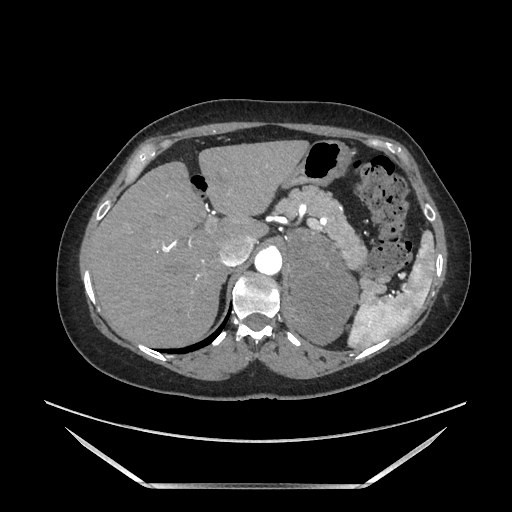
Contrast-enhanced abdominal CT, one axial slice; slice 131 of 205 in the series (ordered by position); soft-tissue window (W 400 / L 40 HU); 1.25 mm slice thickness; 512 × 512 image matrix. Female patient. From the clinical record (not read from this slice): diagnosis: adrenocortical carcinoma; tumour side: left adrenal.
Outlined on this slice (semi-automatically segmented with operator editing):
- mass: bounding box <290,230,356,343> (left, top, right, bottom; pixels)